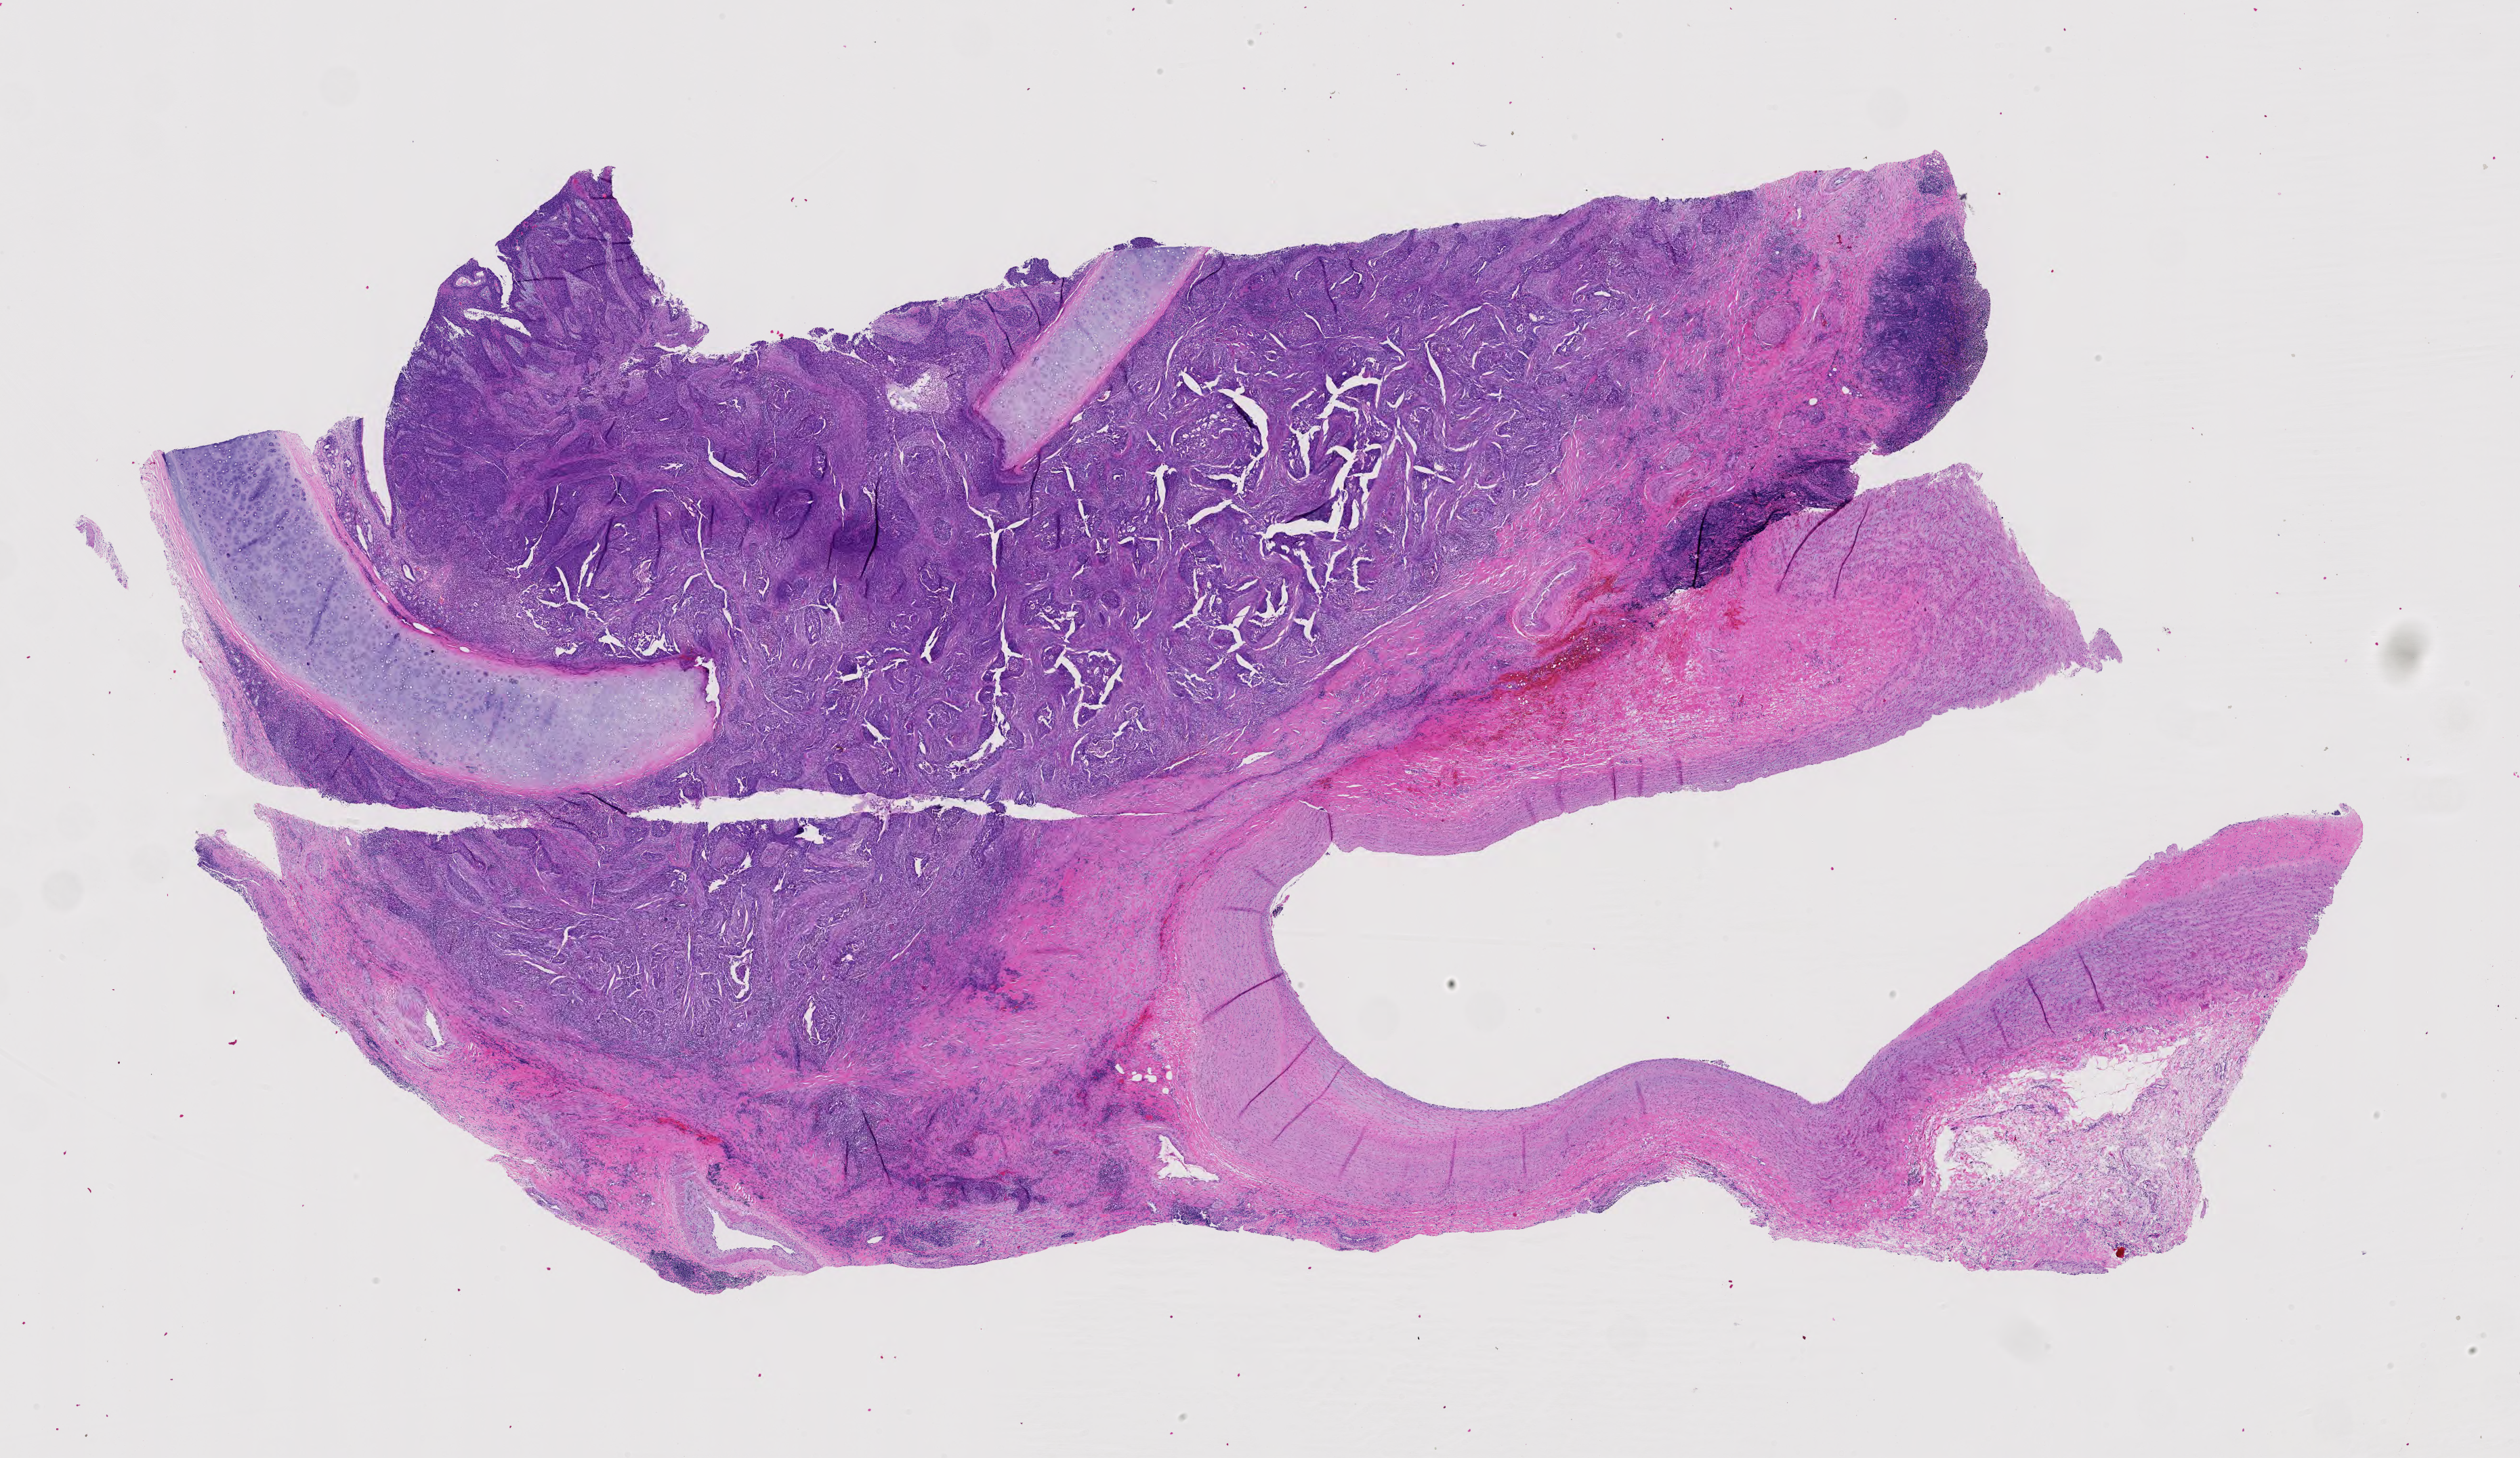
Whole-slide histology image, H&E-stained — a low-resolution overview of the entire scanned area, about 27.0 x 15.6 mm. Formalin-fixed paraffin-embedded (FFPE) diagnostic section. Lung, primary tumour sample. Patient: female, age at initial diagnosis 71 years.
- diagnosis: Squamous cell carcinoma, NOS
- AJCC pathologic stage: IA
- TNM: T1b N0 M0